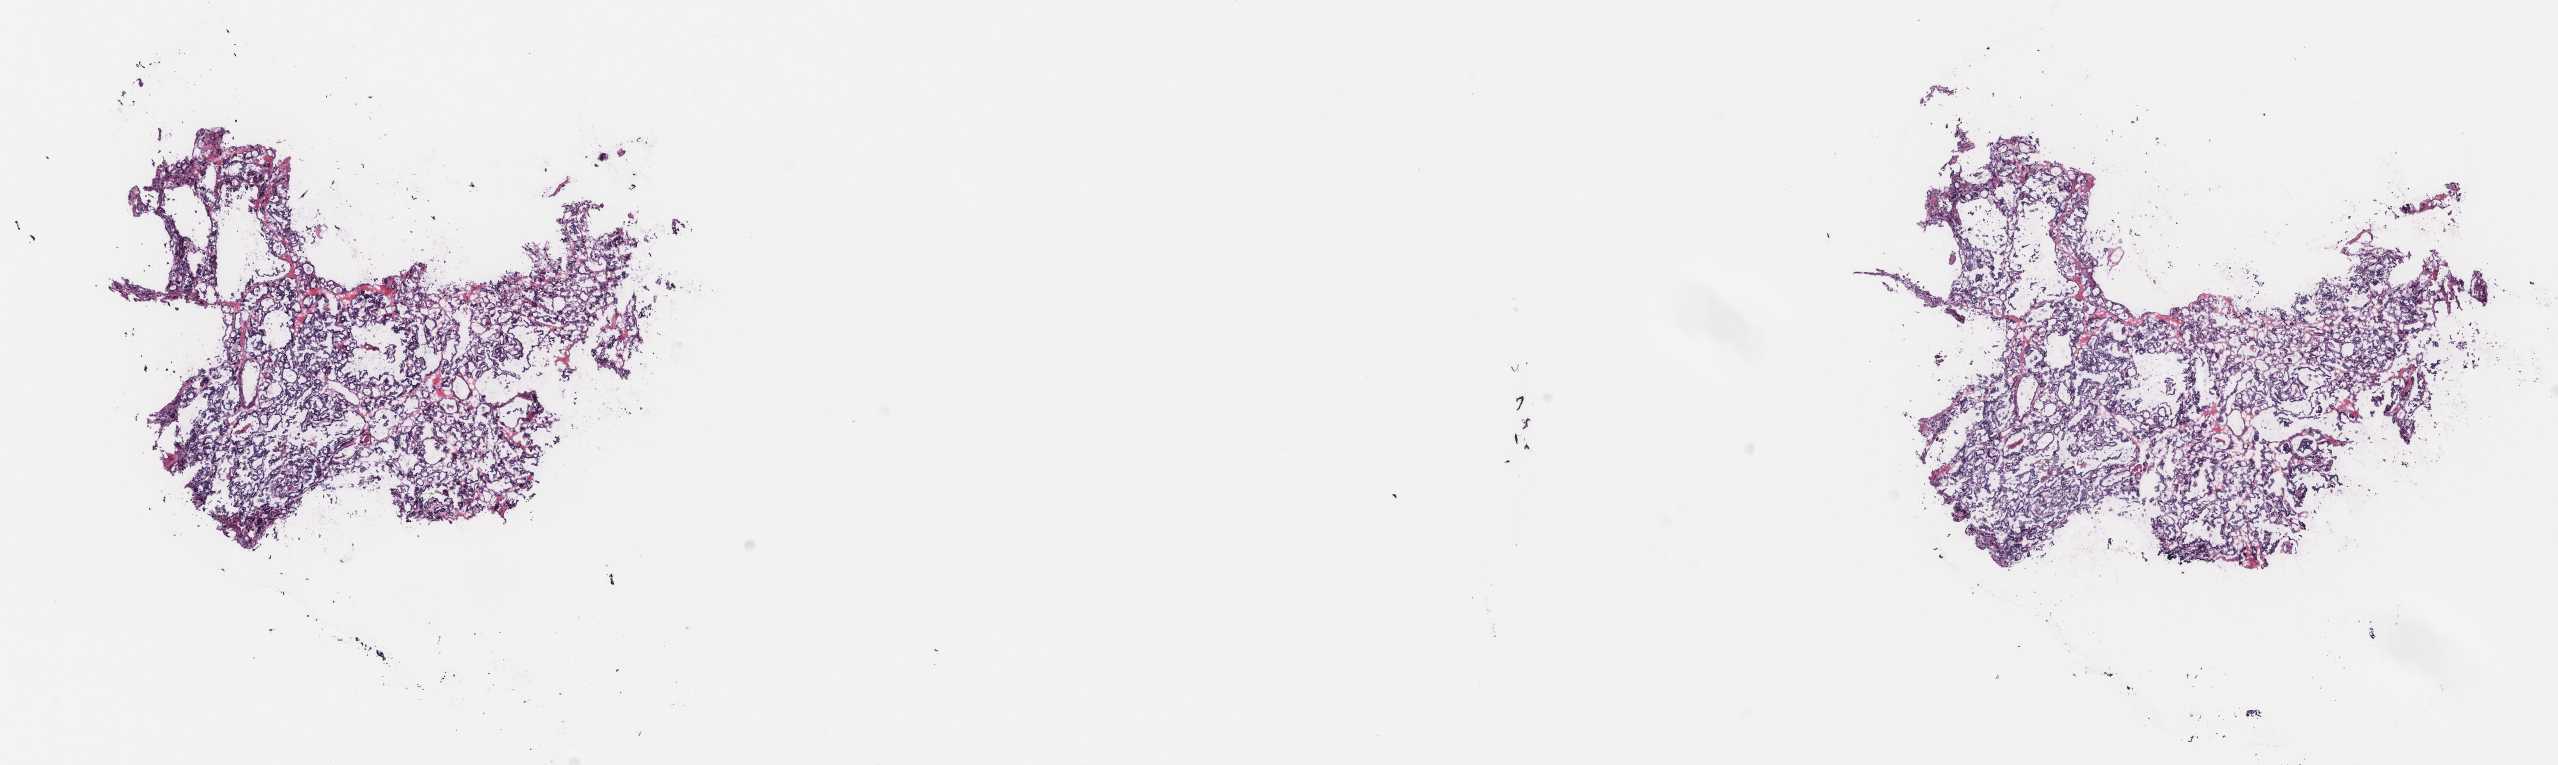
H&E-stained whole-slide image — low-resolution overview of the scanned area, about 20.3 x 6.1 mm. Frozen section from the top of the tissue portion. Thyroid, primary tumour sample. Female patient; age at initial diagnosis 52 years. Slide review estimates, as recorded: tumour cells 100%, tumour nuclei 95%, normal cells 0%, stromal cells 0%, necrosis 0%. Infiltration values recorded for this section: lymphocyte infiltration 0%, monocyte infiltration 0%, neutrophil infiltration 0%.
Diagnosis: Papillary adenocarcinoma, NOS (thyroid gland). AJCC pathologic stage: II (7th edition). Lymph nodes positive (case pathology): 0 of 1 examined.